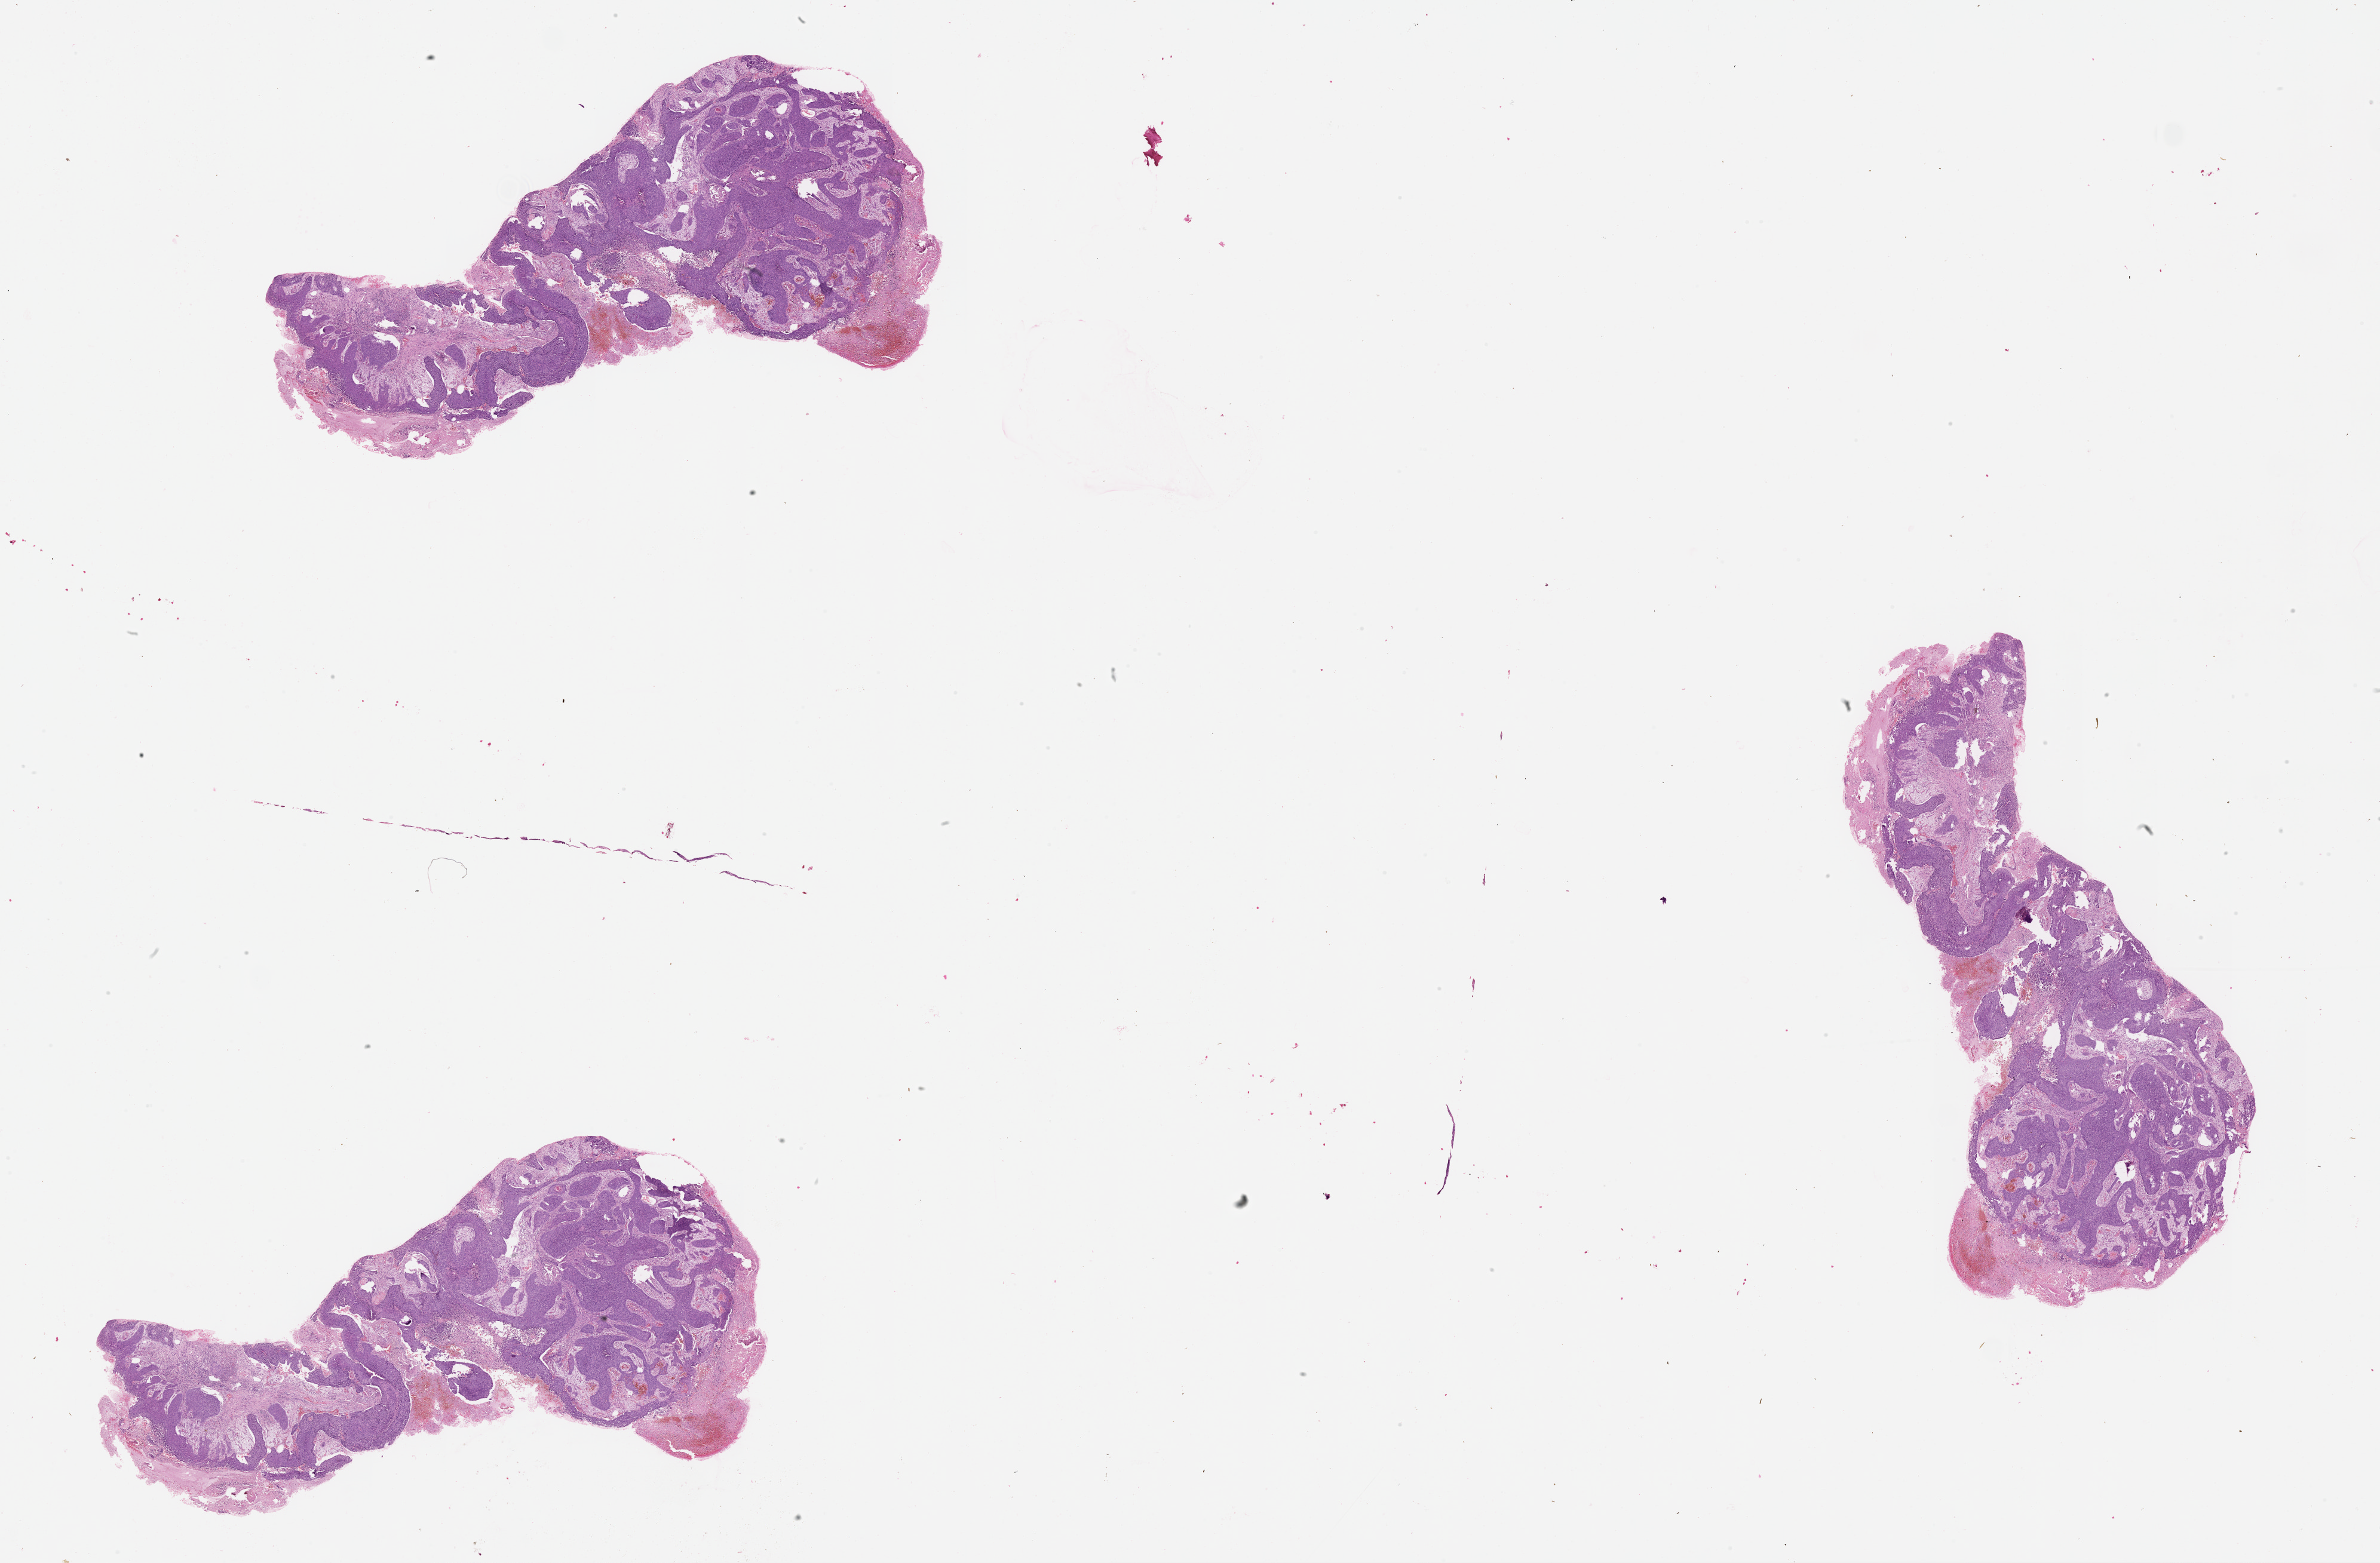
Digitized Hematoxylin and eosin (H&E) stained tissue section (whole slide), whole scanned area (about 32.1 x 21.1 mm, slide scanned at 20x) shown as a low-resolution overview, lung, tumour tissue. Patient: male, age 59 years.
Patient diagnosis (cohort enrolment): squamous cell carcinoma (lung).